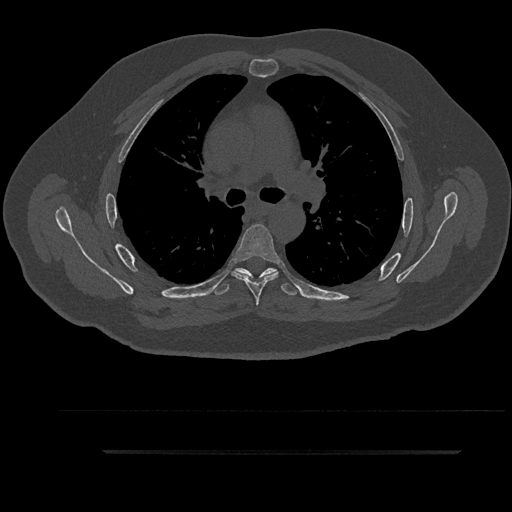
CT including the spine, one axial slice; position 614 of 797 along the scan axis; bone window (W 1800 / L 400 HU); 512 × 512 image matrix, field of view 432 × 432 mm. Patient: male, 63 years. Case-level facts recorded for this patient, not image findings: primary cancer: renal.
Annotated regions visible in this slice (semi-automatically segmented with operator editing):
- T5 vertebra: bounding box <232,224,281,306> (left, top, right, bottom; pixels)
- T6 vertebra: <212,268,298,296>